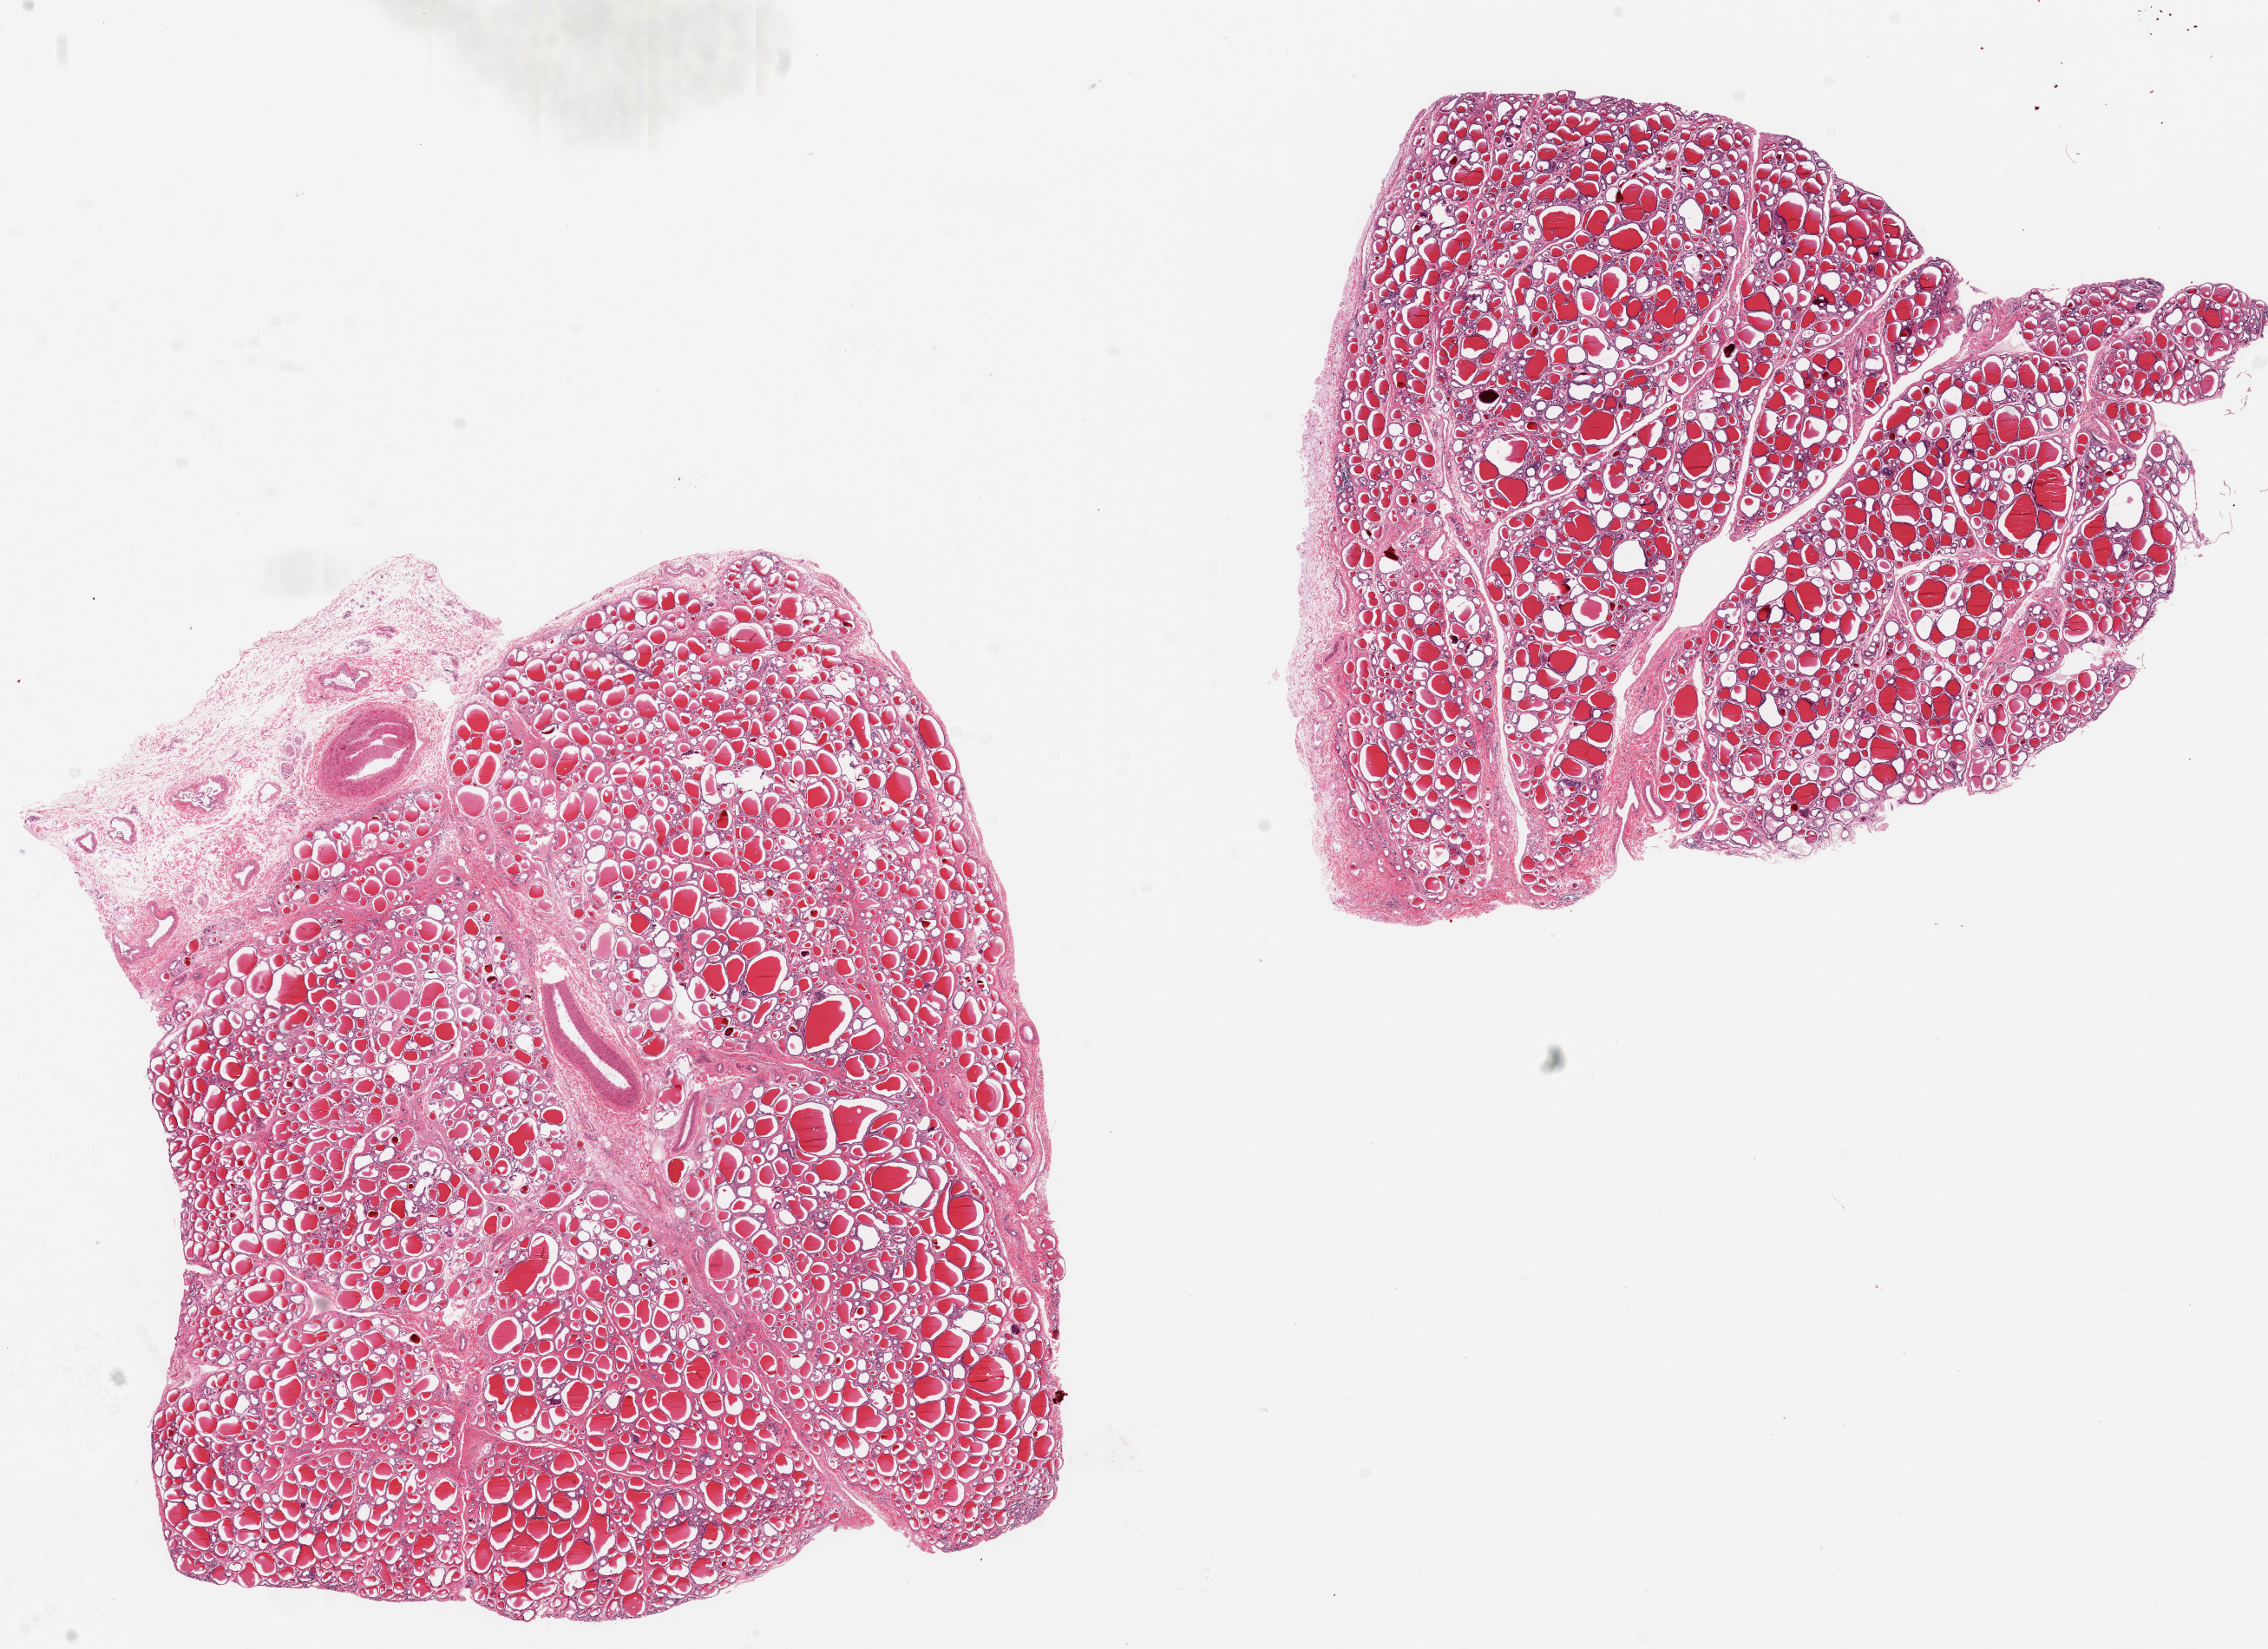
Hematoxylin and eosin (H&E) whole-slide image, brightfield, a low-resolution overview of the entire scanned area, about 20.7 x 15.0 mm; PAXgene-fixed, paraffin-embedded tissue; sampled site (target tissue): thyroid; donor tissue sample. Donor: female.
* reviewer comment on this tissue sample: 2 pieces, 10x8 & 10x8mm; one has nubbine of fat/vascular tissue up to~1.5mm thick